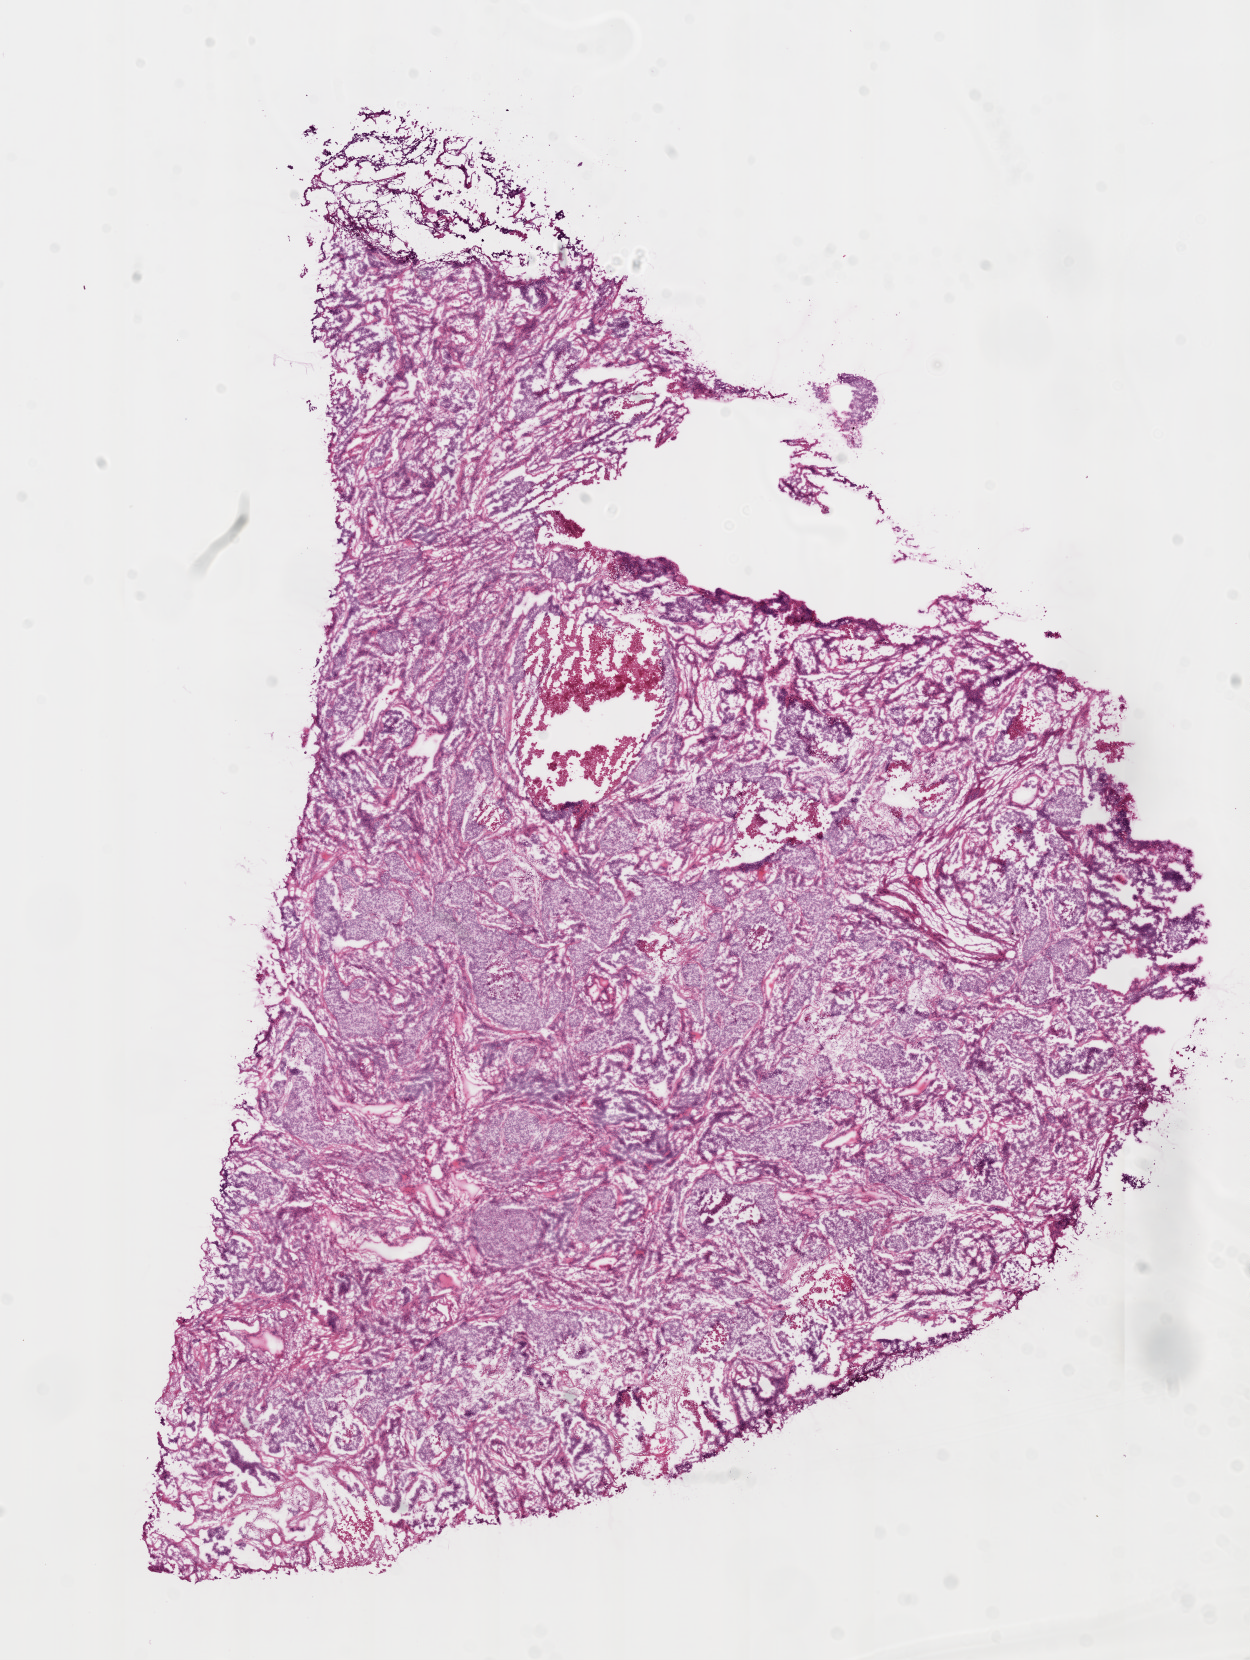
Digitized Hematoxylin and eosin (H&E) stained tissue section (whole slide), shown as a low-resolution overview of the whole scanned area (about 10.0 x 13.3 mm, from a 20x scan). Frozen section. Sample: primary tumour, lung. Male, age 61 years at initial diagnosis. Slide review estimates, as recorded: tumour cells 80%, tumour nuclei 75%, normal cells 0%, stromal cells 15%, necrosis 5%. Infiltration values recorded for this section: lymphocyte infiltration 12%, monocyte infiltration 0%, neutrophil infiltration 0%.
AJCC pathologic stage: IIIA (6th edition). Laterality: left. Diagnosis: Acinar cell carcinoma (lower lobe, lung).